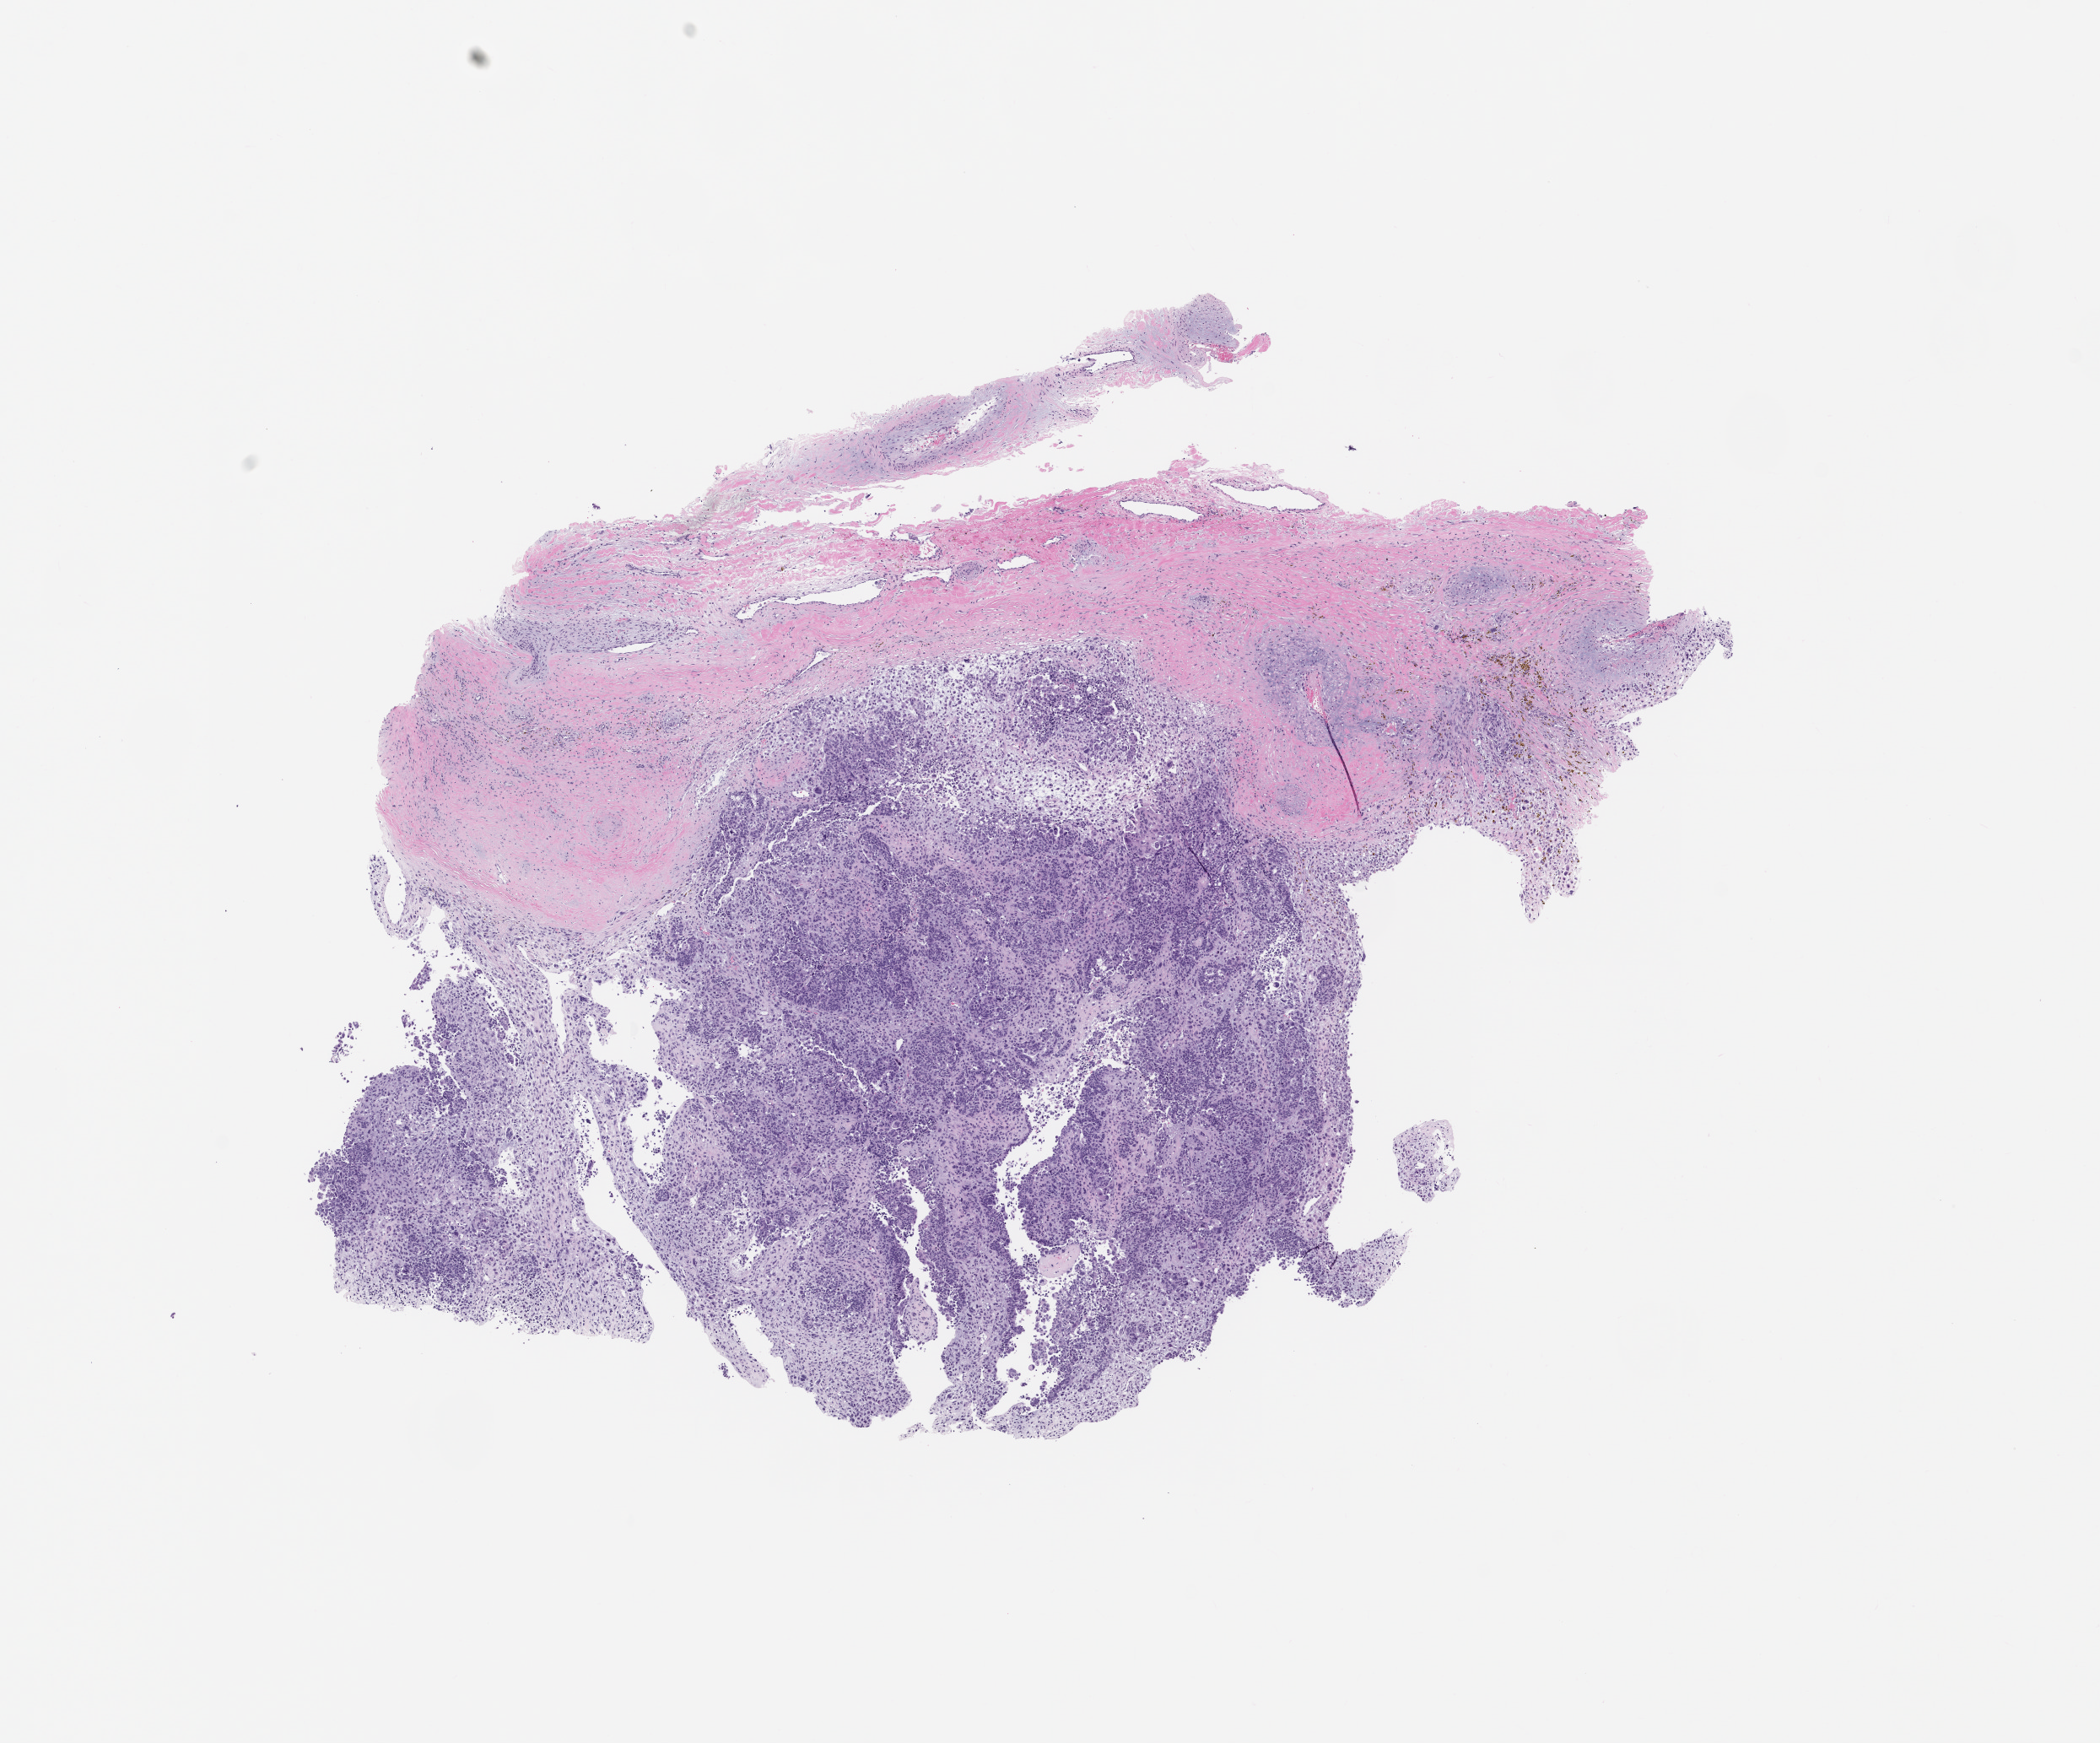
Whole-slide image, haematoxylin and eosin stain of the patient's (originator) tumor tissue, a low-resolution overview of the entire scanned area, about 10.0 x 8.3 mm, formalin-fixed, paraffin-embedded (FFPE) tissue, tumor site category: female genital tract. Female patient, 27 years old.
Diagnosis: Carcinosarcoma.